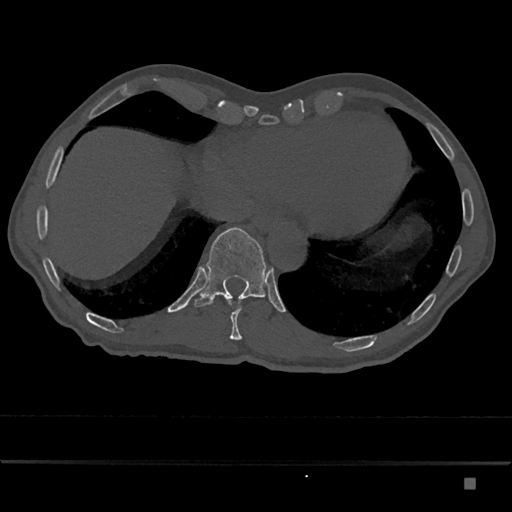
CT including the spine, one axial slice; slice 703 of 797 in the series (ordered by position); 120 kVp; bone window (W 1800 / L 400 HU); 512 × 512 image matrix, field of view 390 × 390 mm. Male patient, age 72 years. Case-level facts recorded for this patient, not image findings: primary cancer: prostate.
Outlined on this slice (semi-automatically segmented with operator editing):
- T10 vertebra: box from (x=226, y=298) to (x=242, y=340) px
- T11 vertebra: (x=193, y=227)–(x=267, y=307)